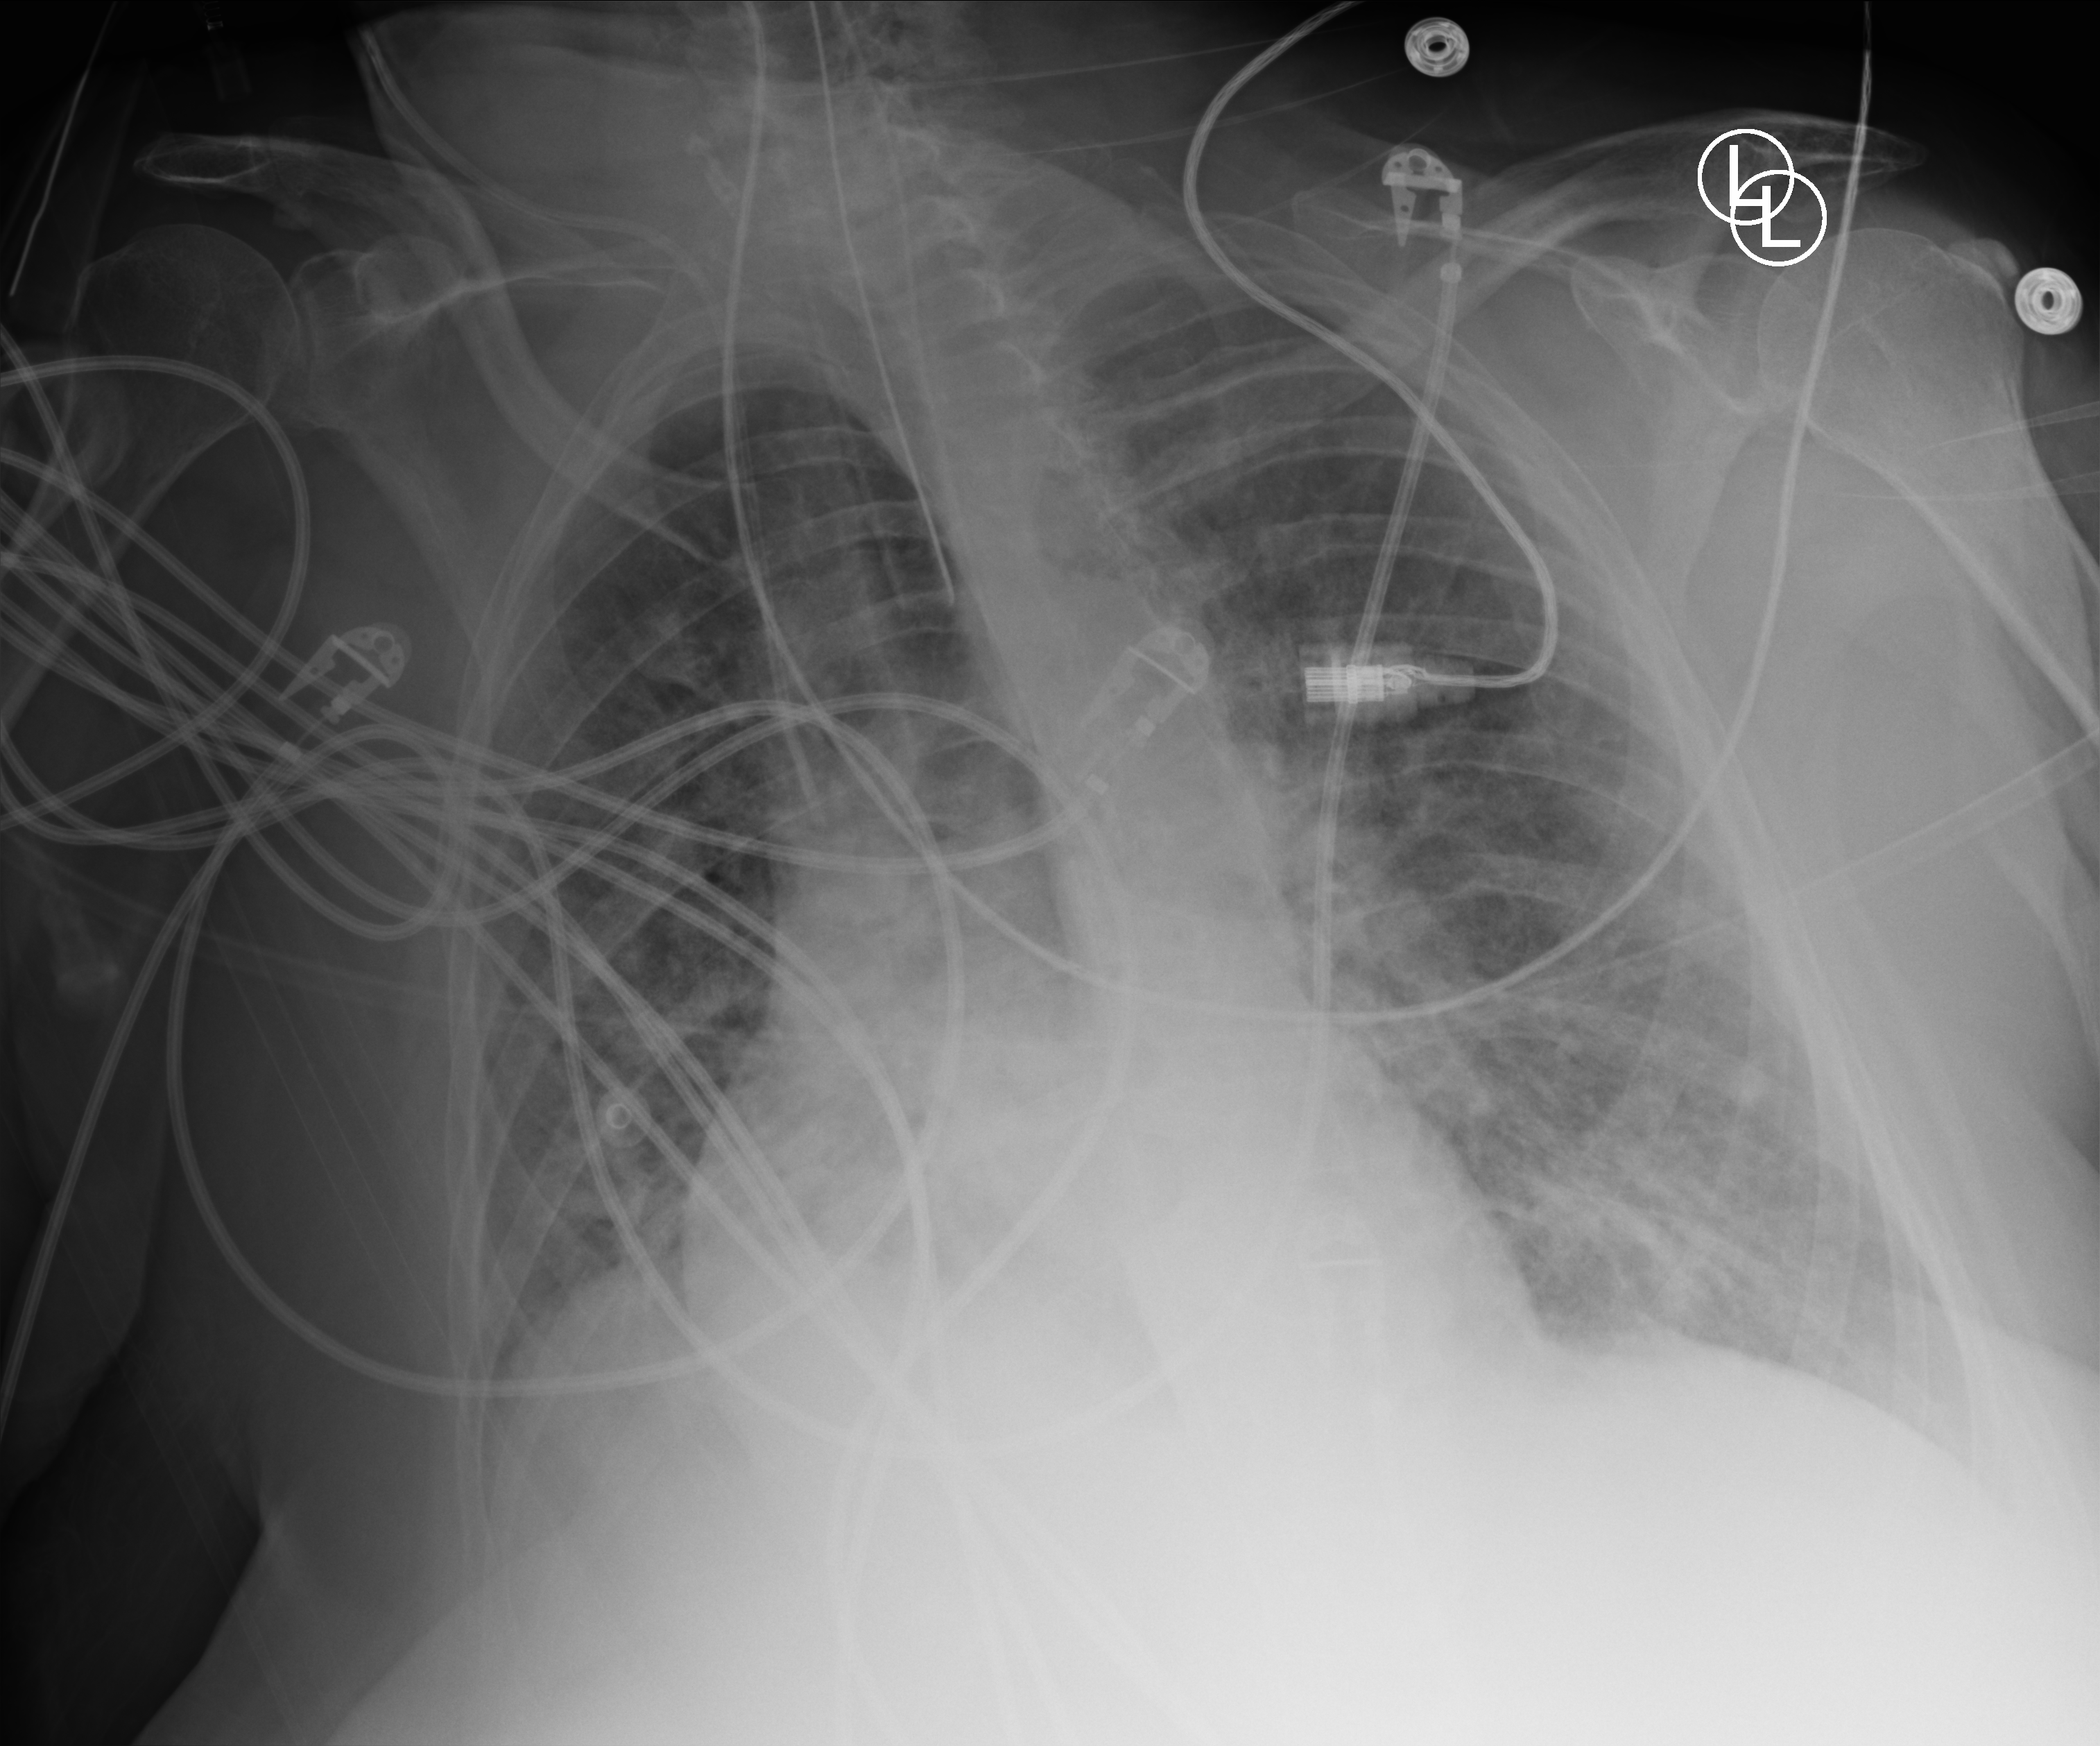
Portable chest radiograph; anteroposterior (AP) projection. Patient hospitalised with COVID-19; female, aged 75–90 years.
Admission-level facts for this patient (not findings on this image; timing relative to this image not recorded):
- other chronic lung disease (admission record): yes
- mechanically ventilated during this hospital stay: yes